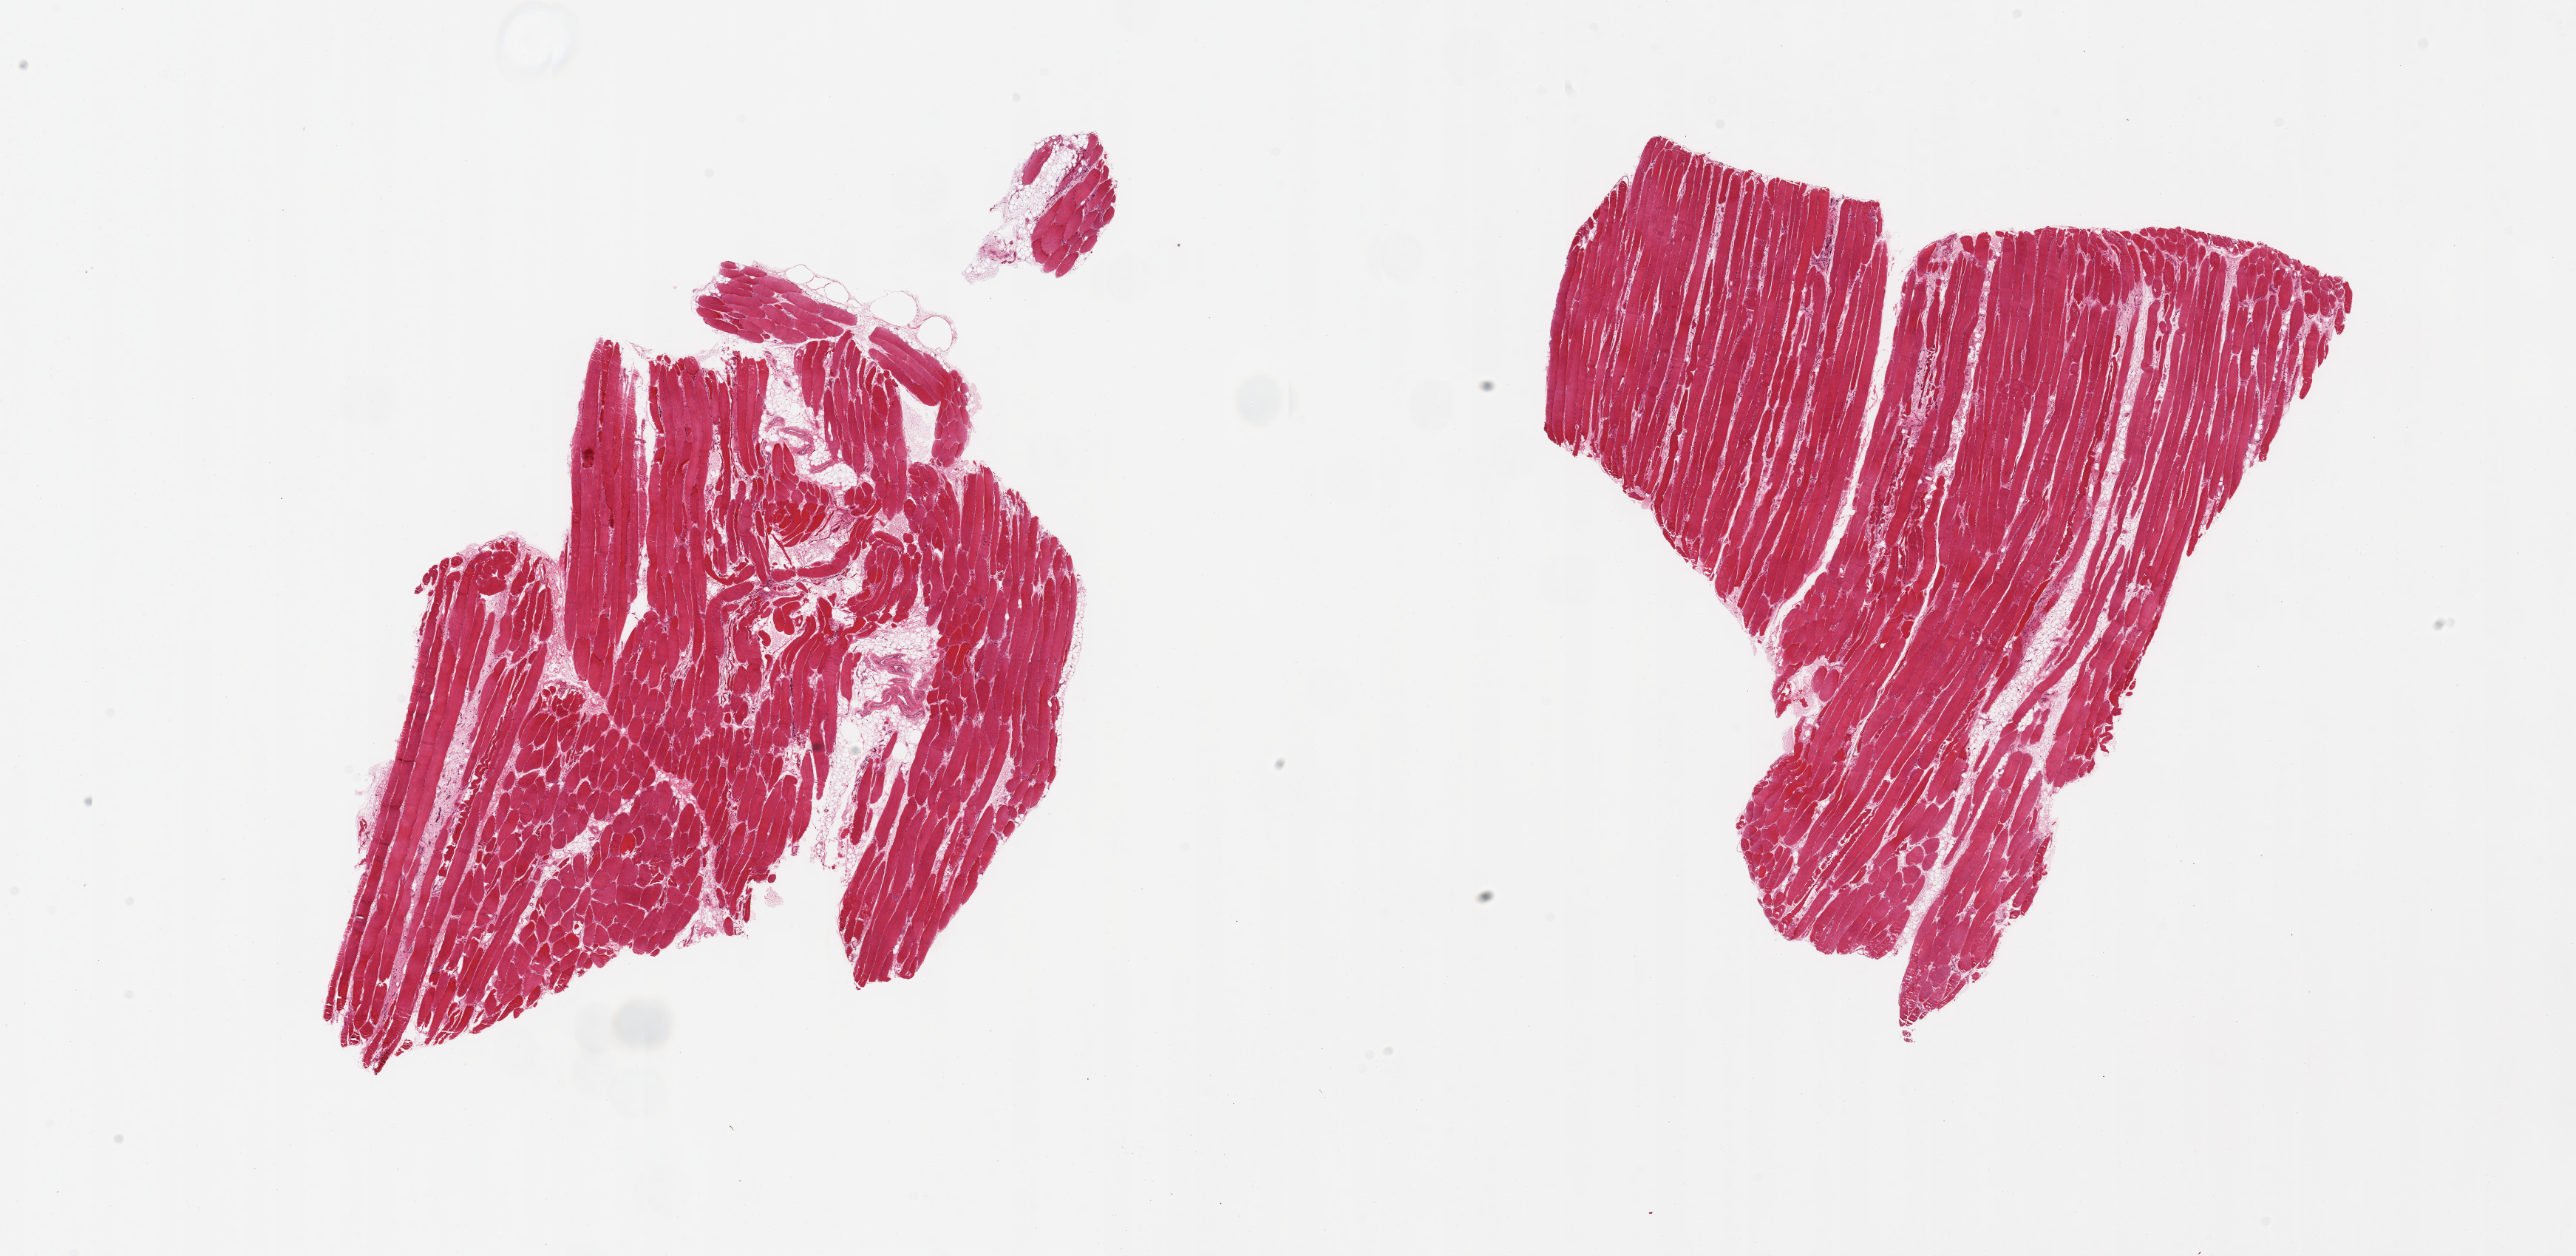
Digitized H&E-stained section — a low-resolution overview of the entire scanned area, about 27.6 x 13.4 mm, PAXgene-fixed, paraffin-embedded tissue, target tissue: skeletal muscle, donor tissue sample. Donor: male.
• review note (as recorded): 2 pieces, ~20-25% interstitial fat